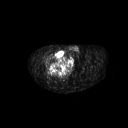
FDG PET of an extremity soft-tissue mass (from a PET/CT study), one axial slice. Slice 275 of 311 in the series (ordered by position). 3.27 mm slice thickness. 128 × 128 image matrix. Patient: male, 50 years. Case-level facts recorded for this patient, not image findings: histological type: undifferentiated - pleiomorphic; grade: high; site of the primary tumour: right thigh.
Structures marked on this image (expert contour drawn on MRI and transferred to this co-registered scan by the dataset authors):
- gross tumour volume including surrounding oedema: bounding box <47,50,66,69> (left, top, right, bottom; pixels)
- gross tumour volume (mass): <47,50,66,69>